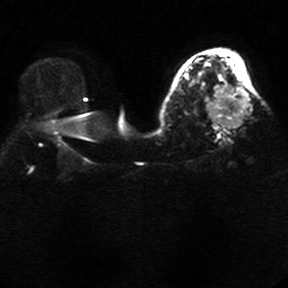
Breast MRI, one axial slice. Position 18 of 34 along the scan axis. Diffusion-weighted series; image 2 of 4 stored at this slice position (different b-values; order by instance number). 1.5 T. 5 mm slice thickness. 288 × 288 image matrix, field of view 340 × 340 mm. Female patient.
Annotated regions visible in this slice (manually delineated by an expert):
- tumour on diffusion-weighted imaging: bounding box <207,86,249,126> (left, top, right, bottom; pixels)